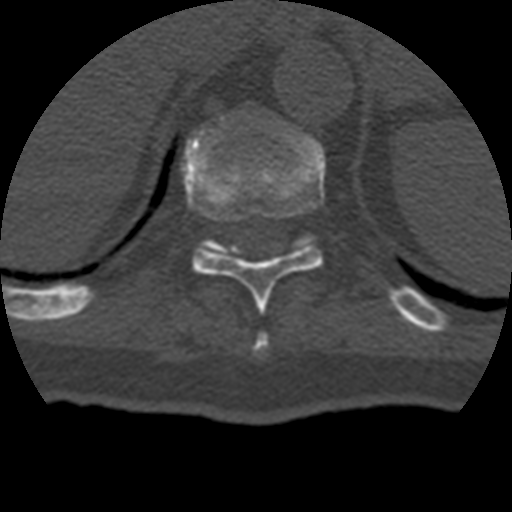
CT including the spine, one axial slice; slice 213 of 399 in the series (ordered by position); reconstruction kernel STANDARD; 120 kVp; bone window (W 1800 / L 400 HU); 1.25 mm slice thickness; 512 × 512 image matrix, field of view 160 × 160 mm. Patient age 69 years. From the clinical record (not read from this slice): primary cancer: prostate.
Outlined on this slice (semi-automatic segmentation, software-assisted and operator-edited):
- T10 vertebra: bounding box [x1, y1, x2, y2] px = [184, 134, 326, 312]
- T11 vertebra: [205, 230, 318, 250]
- T9 vertebra: [254, 333, 269, 352]